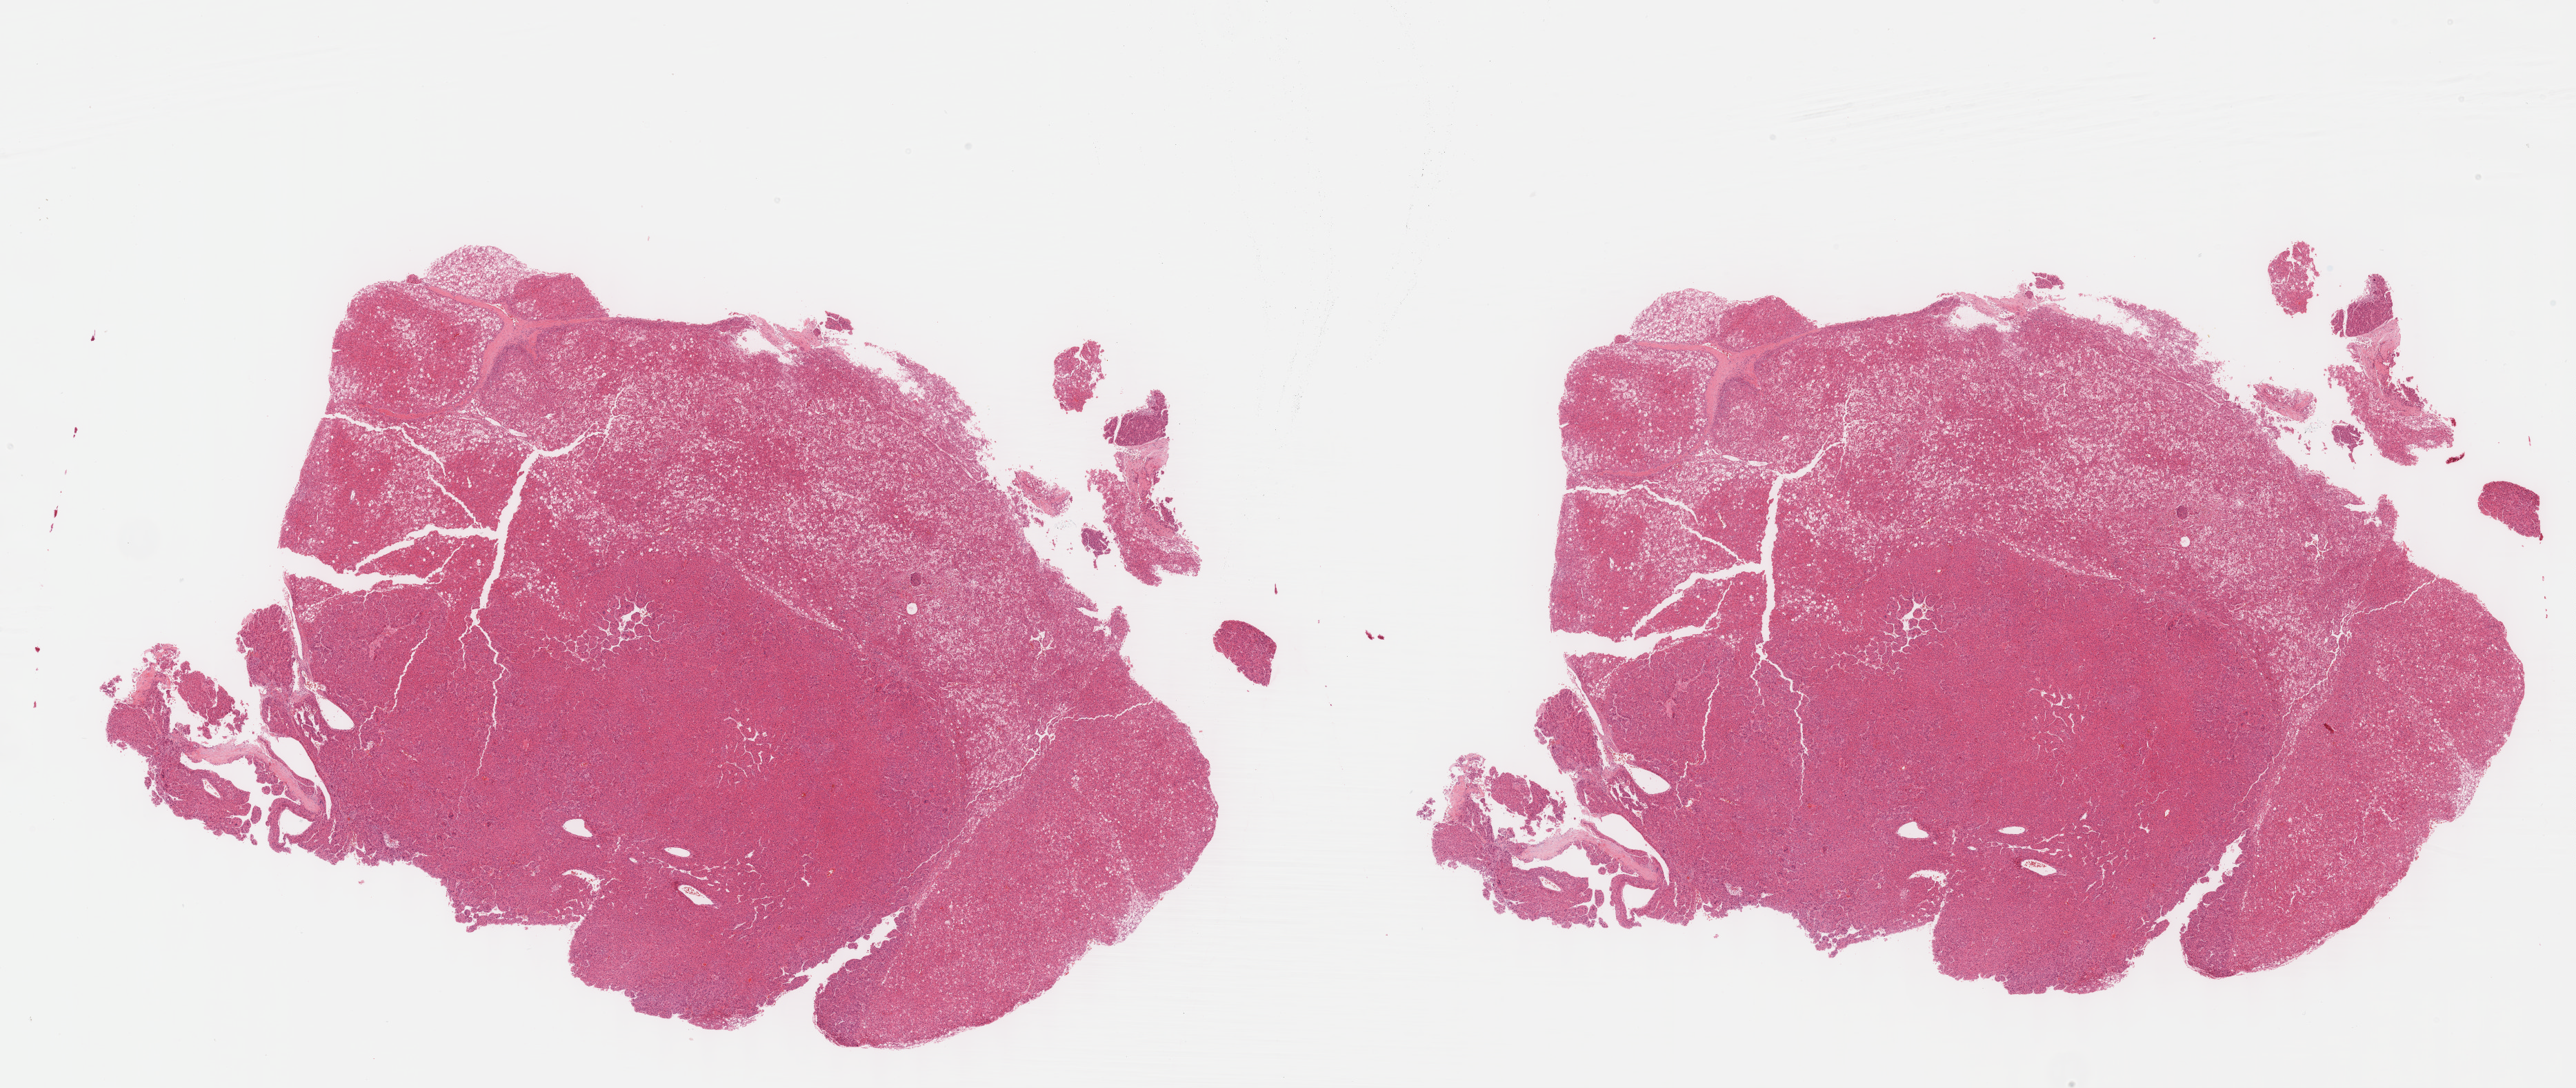
Whole-slide histology image, H&E, low-resolution overview of the scanned area, about 30.2 x 12.7 mm (slide scanned at 40x); formalin-fixed paraffin-embedded (FFPE) diagnostic section; liver, primary tumour sample. Male patient; age at initial diagnosis 75 years.
Diagnosis: Hepatocellular carcinoma, NOS.